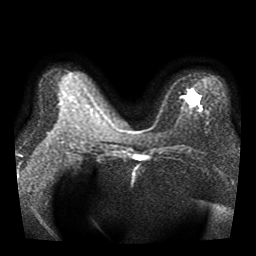
Breast MRI, one axial slice; position 20 of 40 along the scan axis; diffusion-weighted series; image 2 of 4 stored at this slice position (different b-values; order by instance number); 1.5 T; 256 × 256 image matrix, field of view 330 × 330 mm. Female patient.
Annotated regions visible in this slice (expert manual segmentation):
- tumour on diffusion-weighted imaging: bounding box (x1, y1, x2, y2) in pixels: (184, 89, 201, 106)